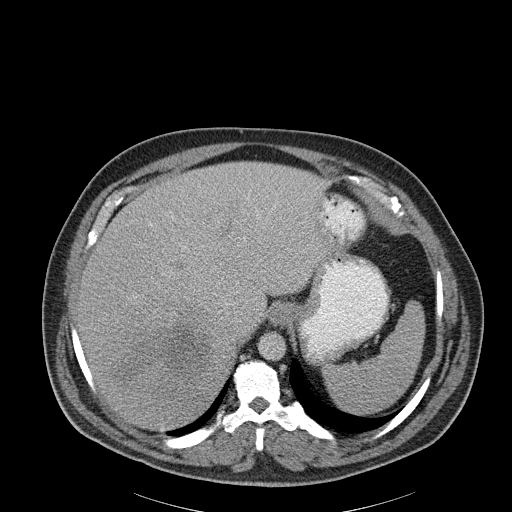
Contrast-enhanced abdominal CT, one axial slice. Position 151 of 186 along the scan axis. 120 kVp. Soft-tissue window (W 400 / L 40 HU). 512 × 512 image matrix, field of view 464 × 464 mm. Male patient, age 56 years. From the clinical record (not read from this slice): diagnosis: adrenocortical carcinoma; tumour side: right adrenal; tumour size at pathology: 18 cm; Ki-67 index: 2 %.
Outlined on this slice (semi-automatically segmented with operator editing):
- mass: bounding box [x1, y1, x2, y2] px = [115, 325, 205, 381]